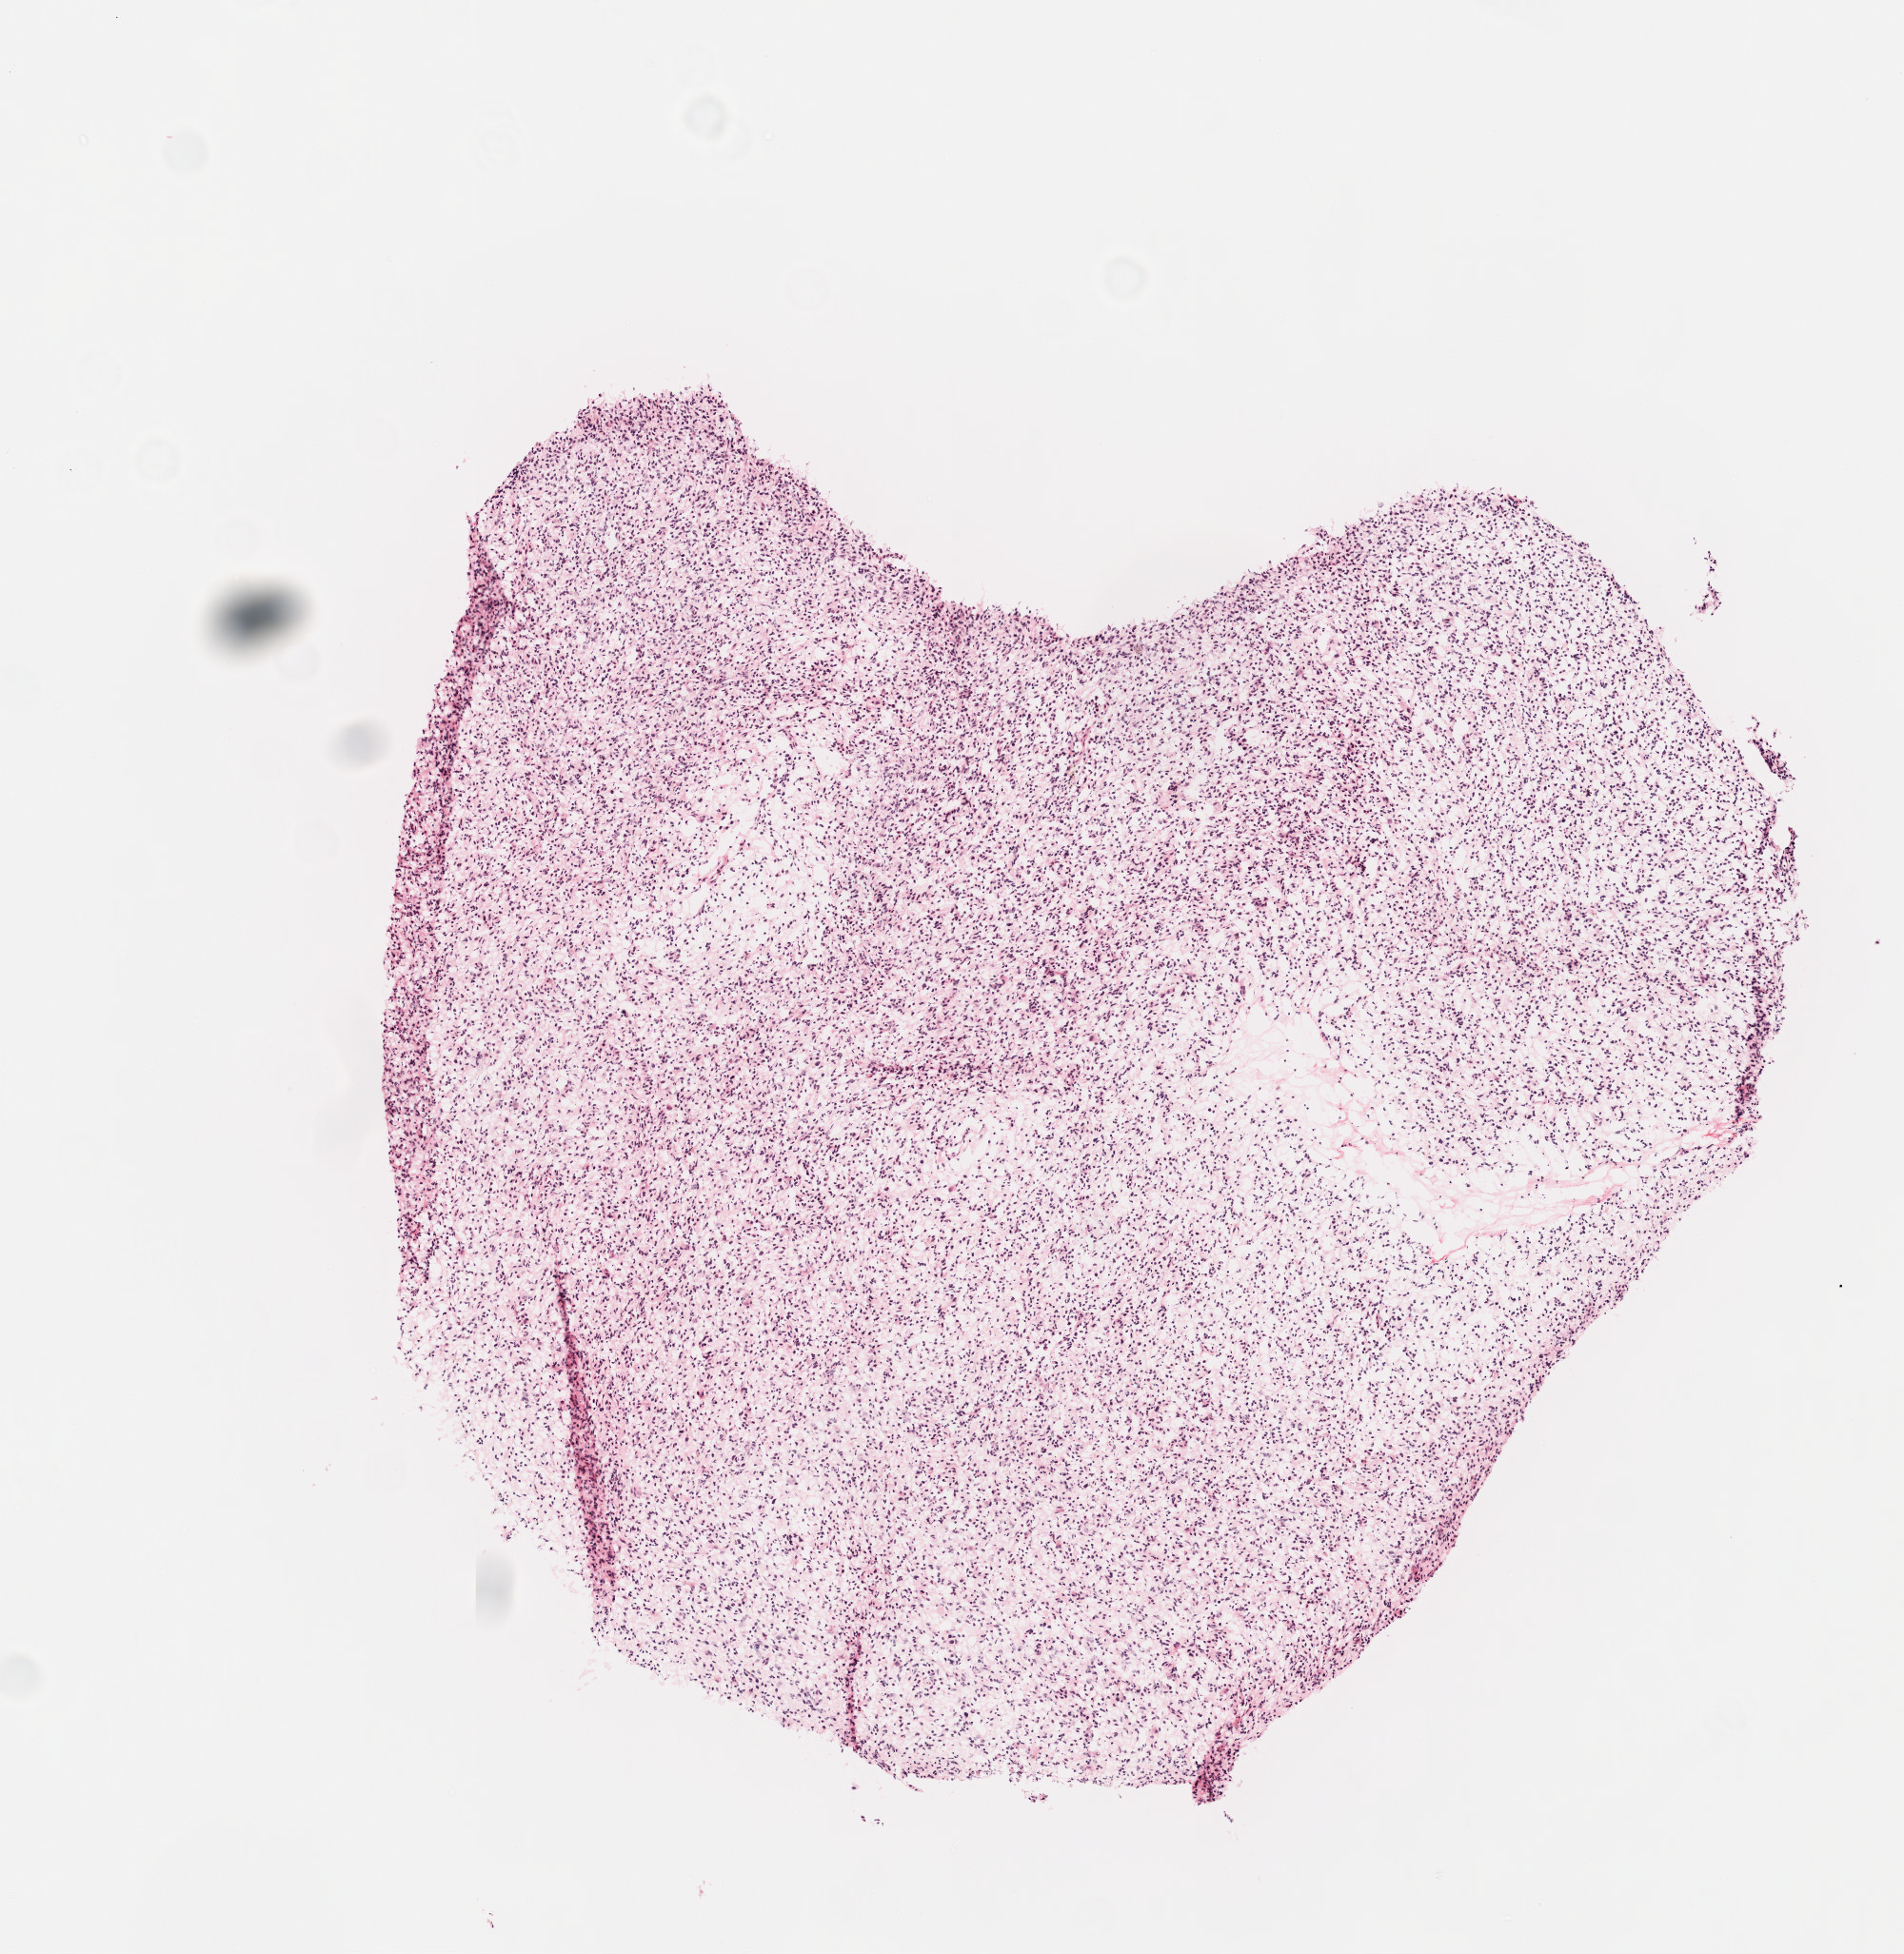
H&E whole-slide image, shown as a low-resolution overview of the whole scanned area (about 4.0 x 4.1 mm, from a 20x scan); frozen section; primary tumour sample from the brain. Male patient; age at initial diagnosis 51 years.
Diagnosis: Glioblastoma.